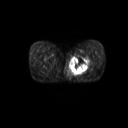
FDG PET of an extremity soft-tissue mass (from a PET/CT study), one axial slice. 3.27 mm slice thickness. 128 × 128 image matrix. Patient: male, 59 years. Case-level facts recorded for this patient, not image findings: histological type: pleiomorphic liposarcoma; grade: high; site of the primary tumour: left thigh.
Annotated regions visible in this slice (expert contour drawn on MRI and transferred to this co-registered scan by the dataset authors):
- gross tumour volume including surrounding oedema: bounding box (x1, y1, x2, y2) in pixels: (70, 55, 92, 75)
- gross tumour volume (mass): (71, 56, 88, 74)